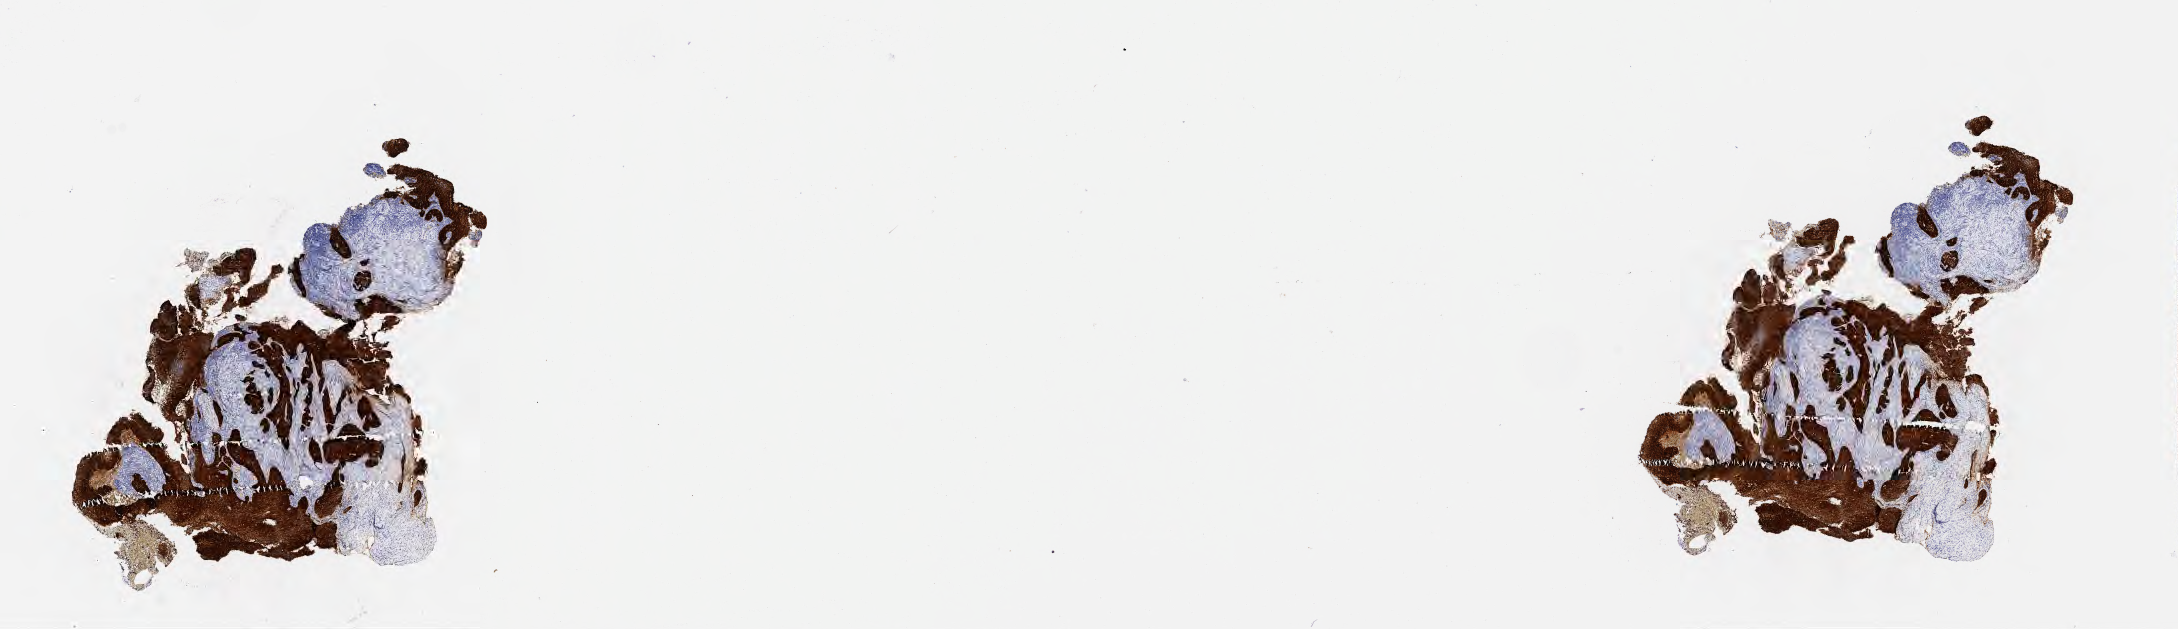
Whole-slide image, immunohistochemical stain for p16 (p16INK4a) — a low-resolution overview of the entire scanned area, about 17.6 x 5.1 mm. Tumor tissue. Site: cervix. Female patient, aged 51.
Histologic diagnosis: Squamous cell carcinoma, large cell, nonkeratinizing, NOS.